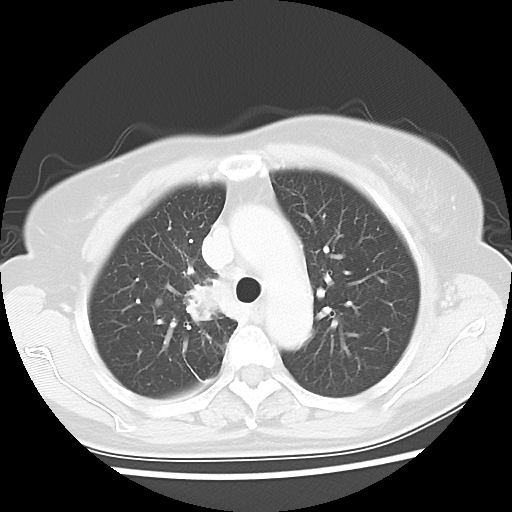
Chest CT, one axial slice; slice 41 of 56 in the series (ordered by position); reconstruction kernel LUNG; lung window (W 1500 / L -600 HU); 5 mm slice thickness; 512 × 512 image matrix, field of view 314 × 314 mm. Patient: female, 62 years. From the clinical record (not read from this slice): clinical TNM (as recorded): T2 N1 M1a.
Annotated regions visible in this slice (bounding box drawn by a radiologist):
- lung tumour (recorded histology: adenocarcinoma): bounding box <176,271,235,326> (left, top, right, bottom; pixels)